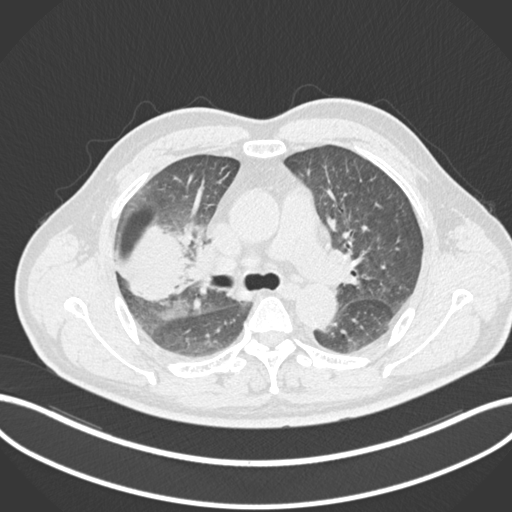
Chest CT, one axial slice. Position 649 of 852 along the scan axis. 120 kVp. Lung window (W 1500 / L -600 HU). 1 mm slice thickness. 512 × 512 image matrix. Patient: male, 55 years. From the clinical record (not read from this slice): clinical TNM (as recorded): T3 N2 M1.
Structures marked on this image (rectangle marked by the reading radiologist):
- lung tumour (recorded histology: adenocarcinoma): bounding box <115,219,189,302> (left, top, right, bottom; pixels)